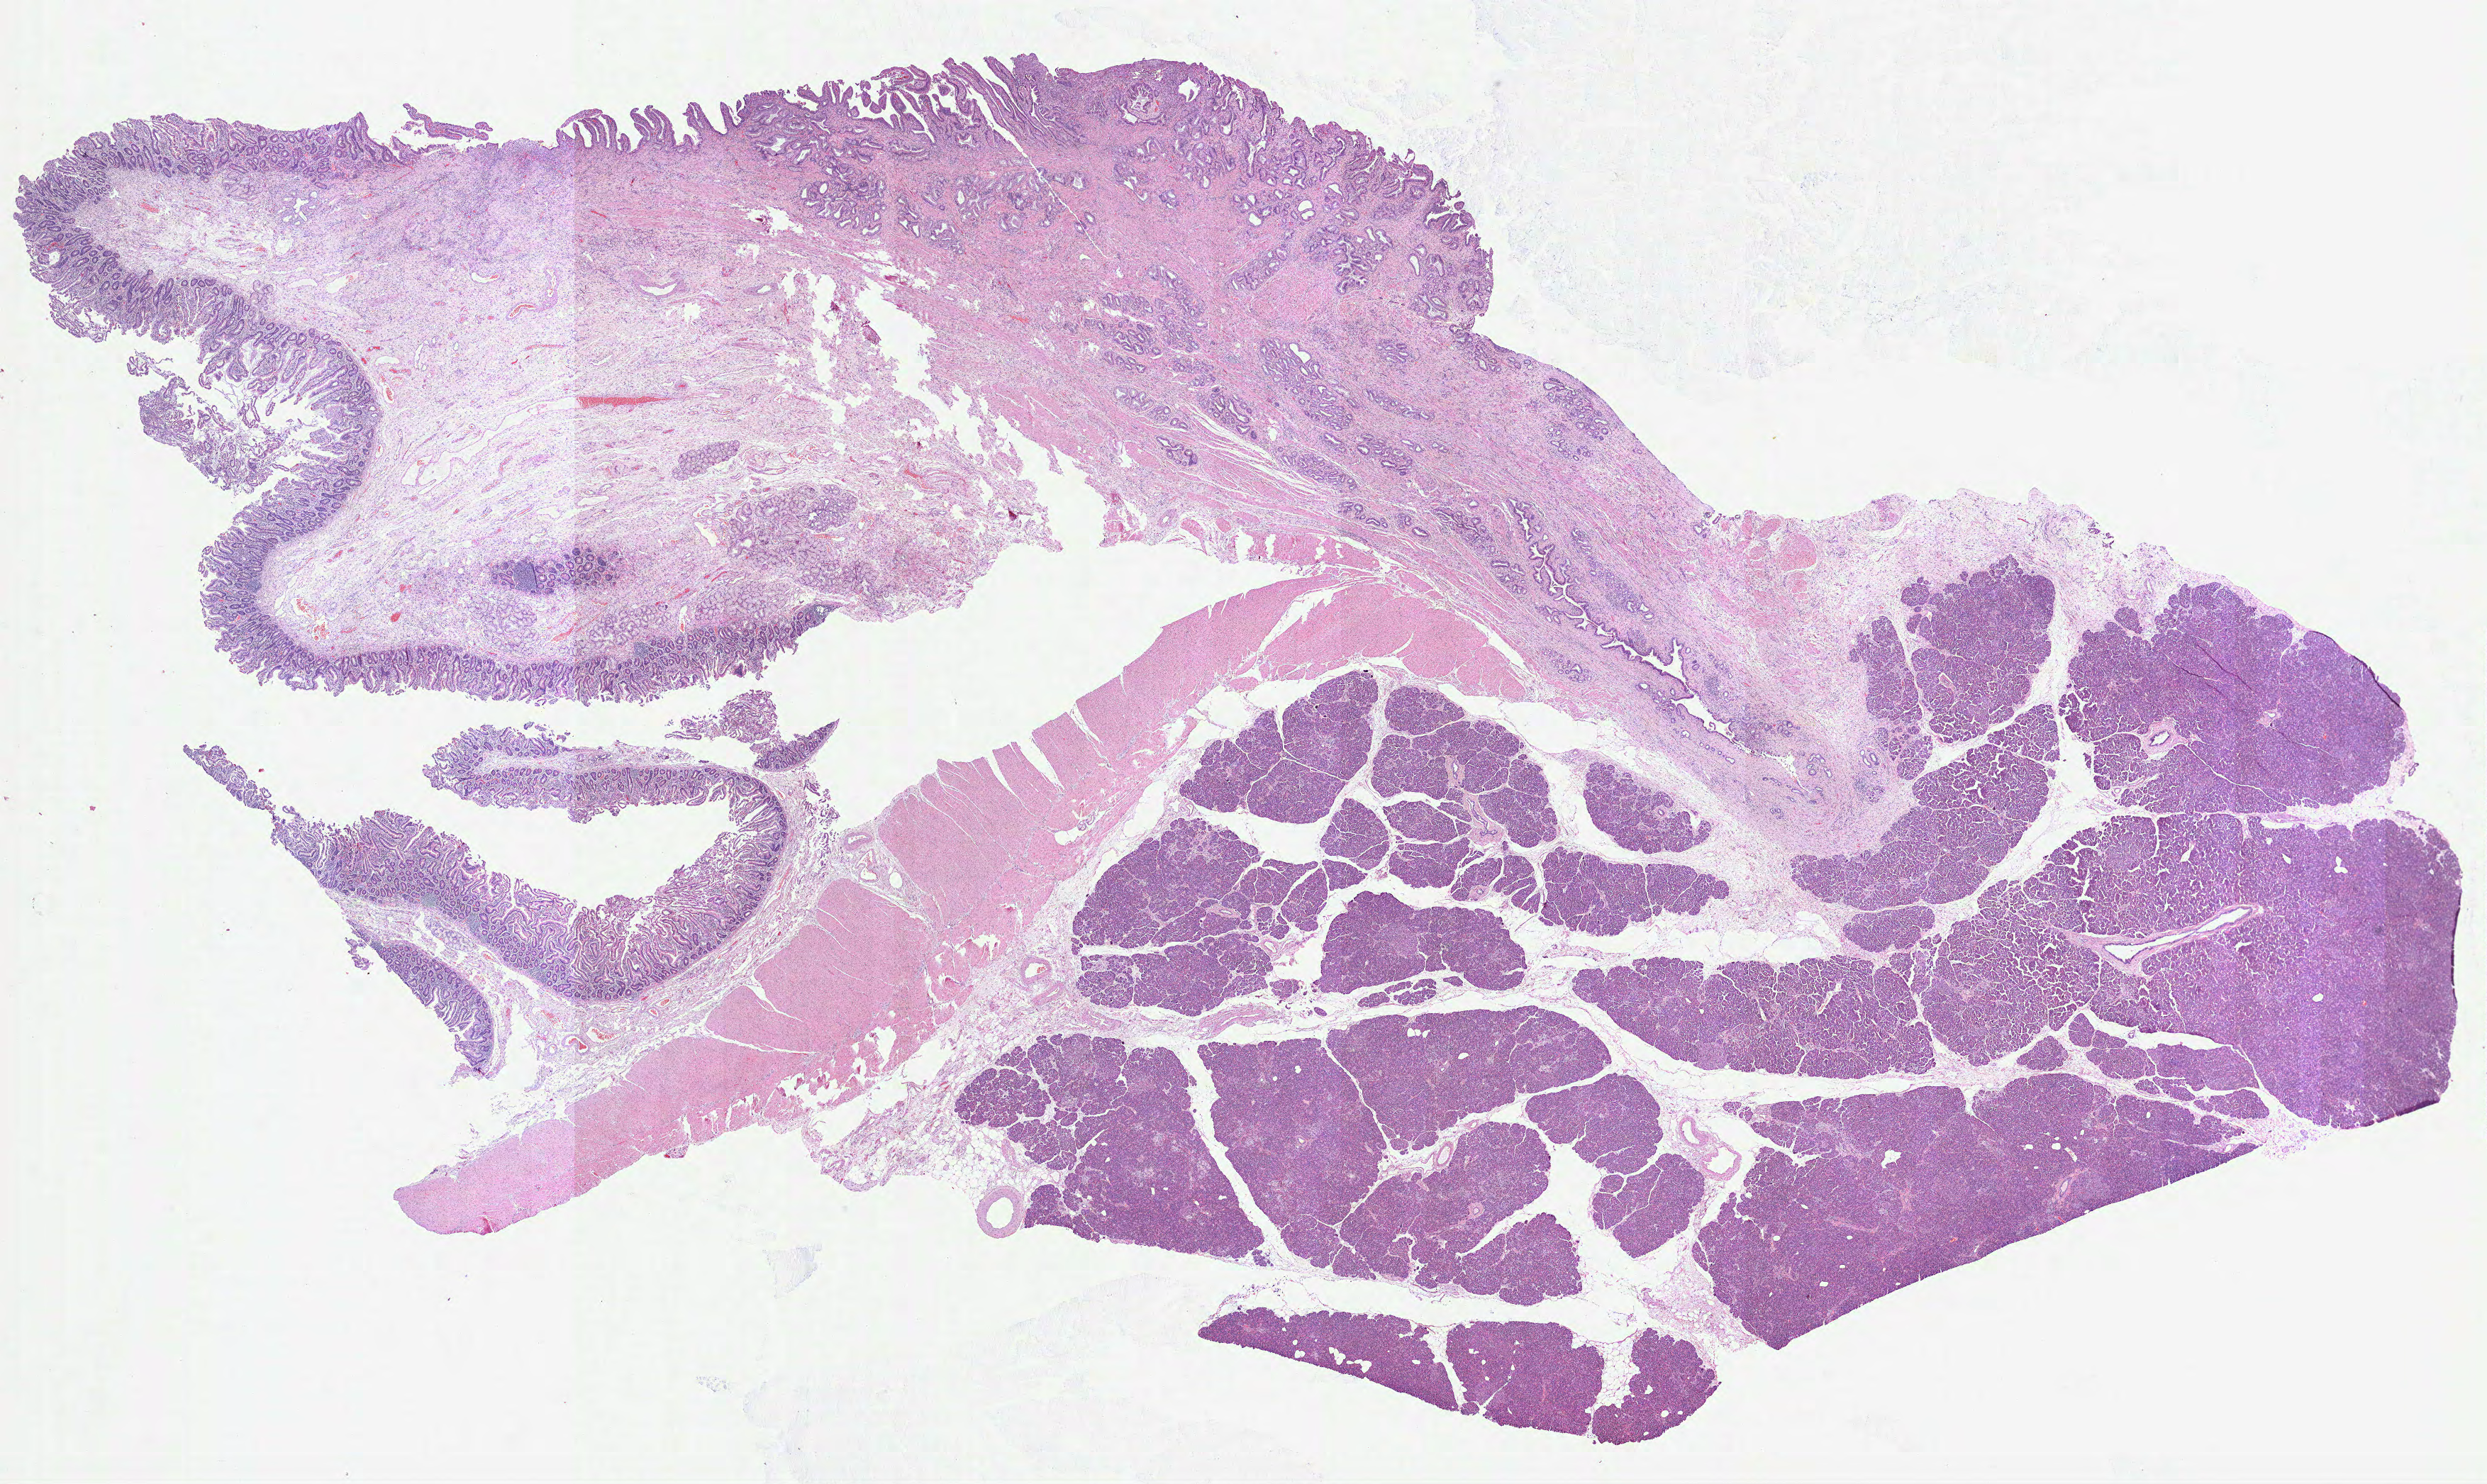
Digitized Hematoxylin and eosin (H&E) stained tissue section (whole slide), a low-resolution overview of the entire scanned area, about 28.3 x 16.9 mm, formalin-fixed paraffin-embedded (FFPE) diagnostic section, pancreas, primary tumour sample. Female patient; age at initial diagnosis 84 years. Histologic grade: GX (grade cannot be assessed).
- diagnosis: Mucinous adenocarcinoma (head of pancreas)
- AJCC pathologic stage: IA